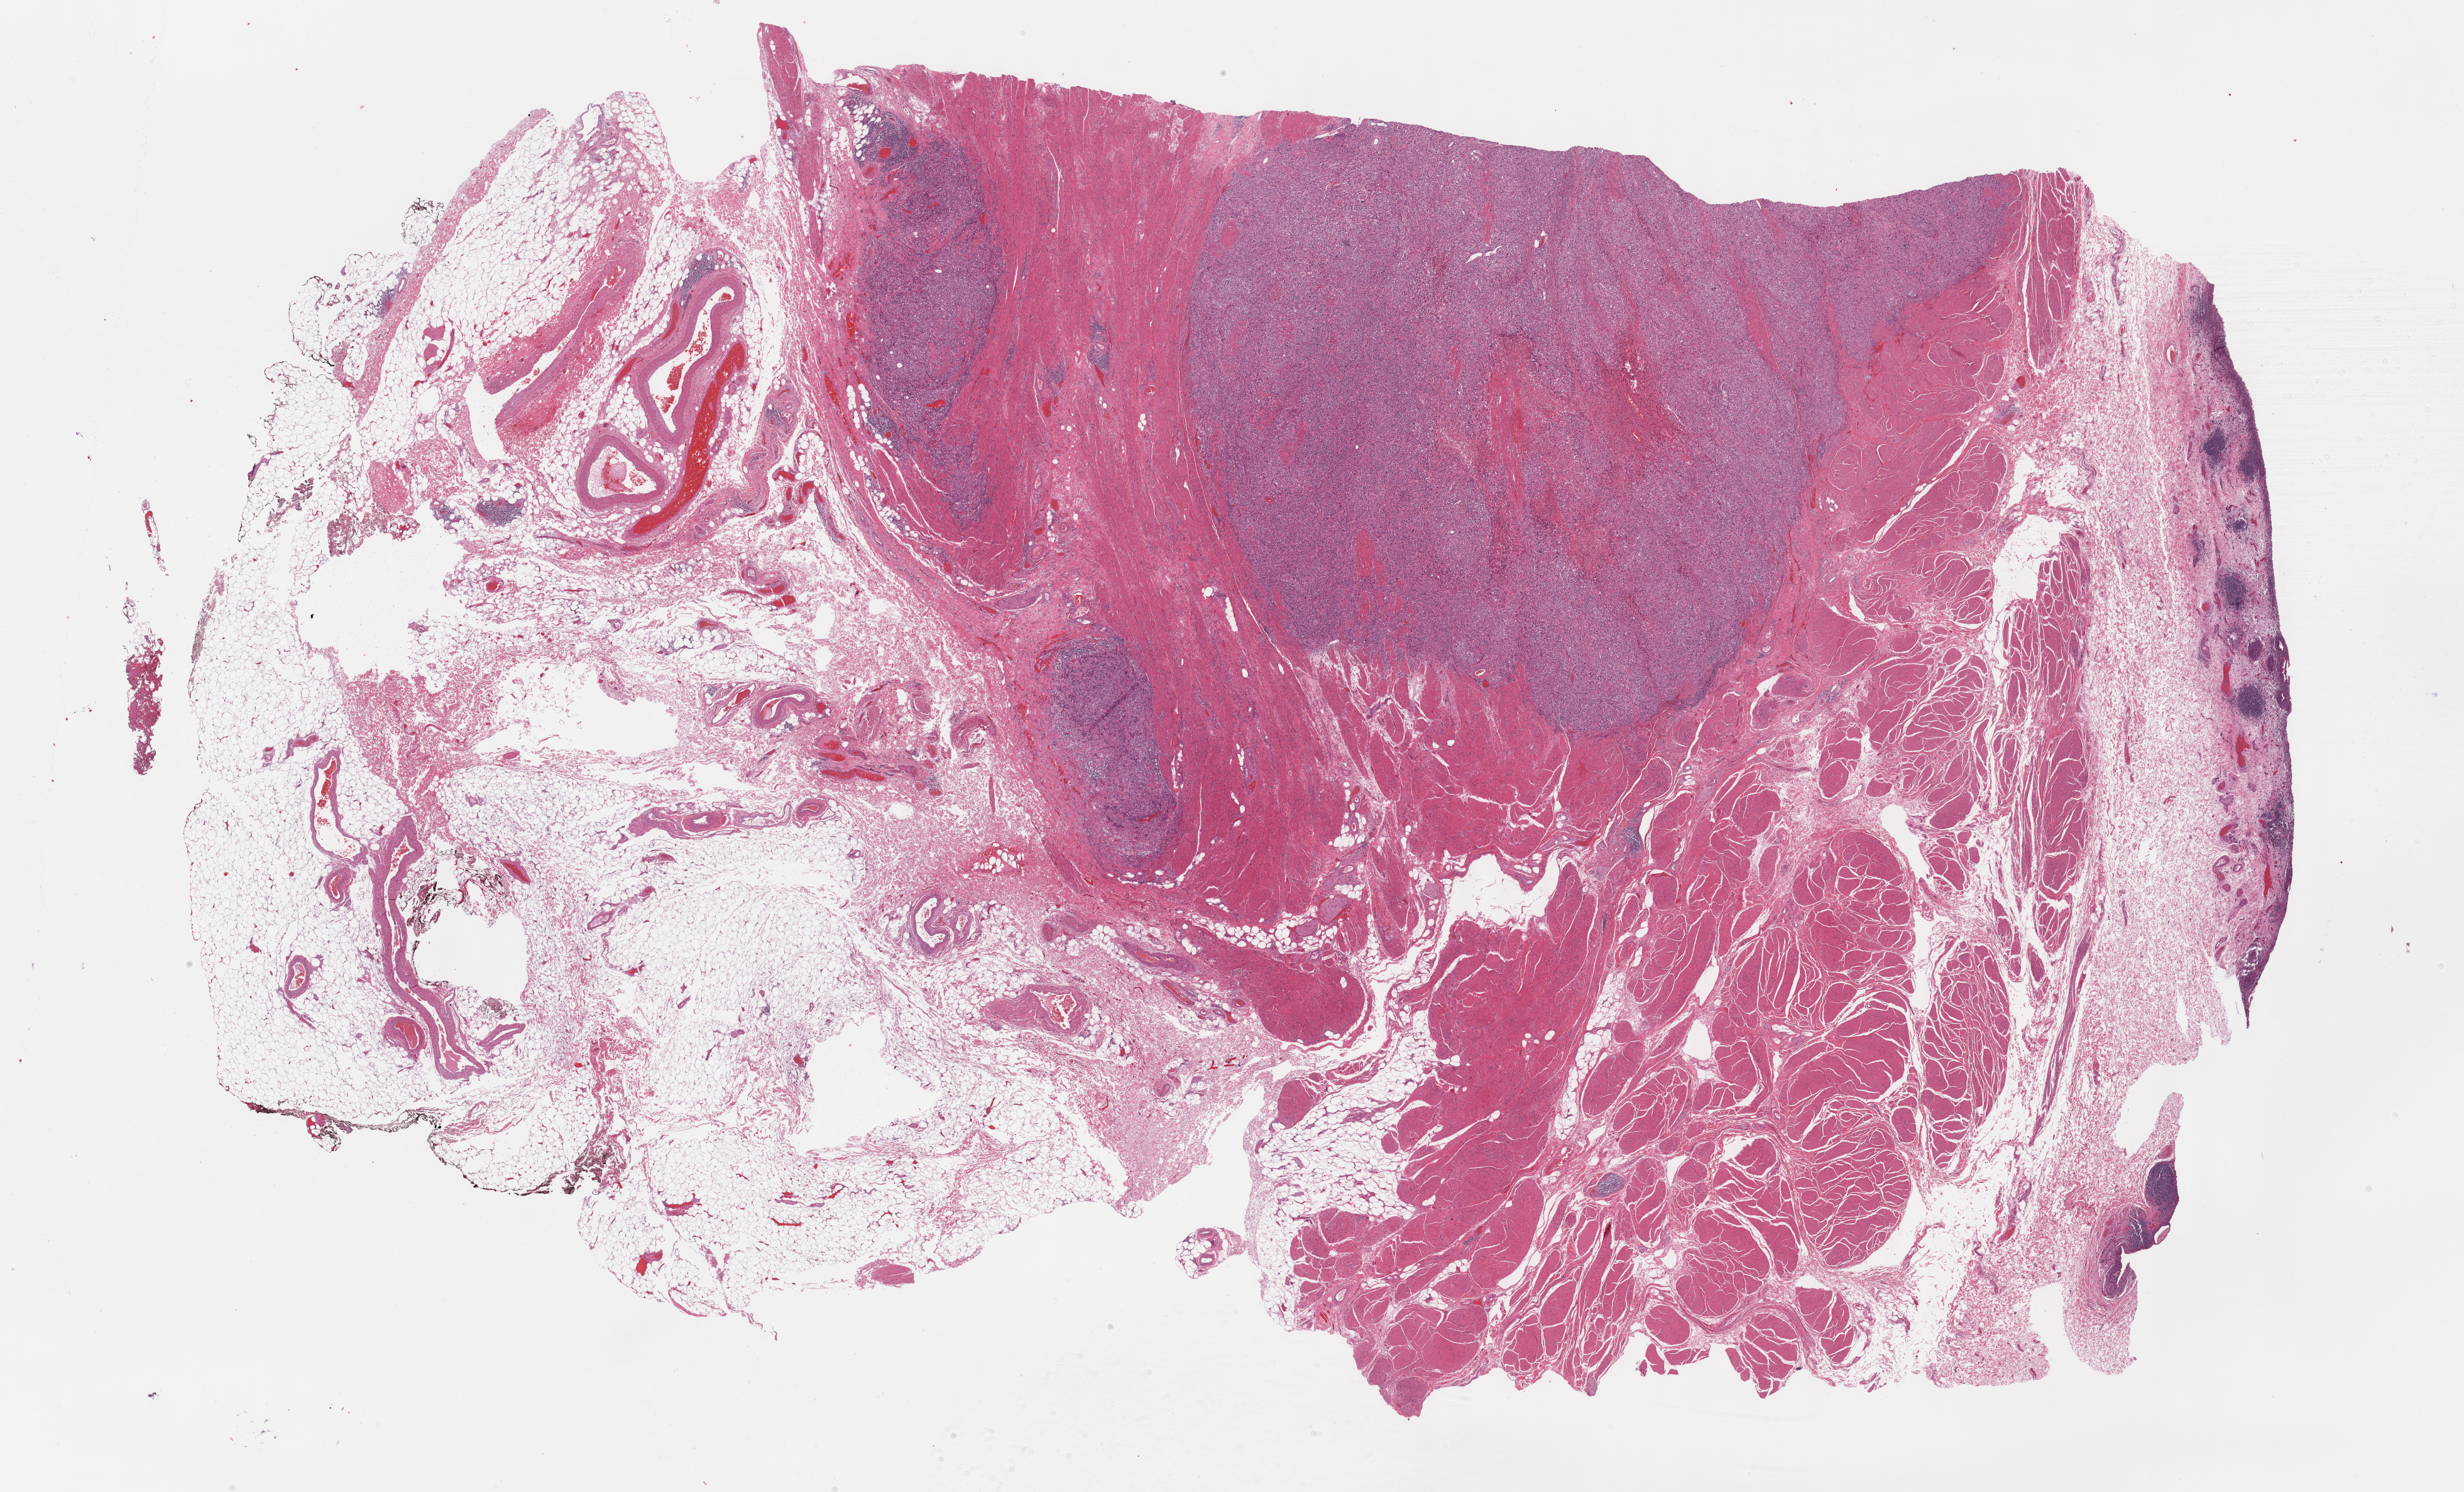
Whole-slide histology image, H&E, a low-resolution overview of the entire scanned area, about 31.7 x 19.2 mm, FFPE section, primary tumour sample from the bladder. Male patient; age at initial diagnosis 84 years. Histologic grade: high grade.
* AJCC pathologic stage: III (7th edition)
* diagnosis: Transitional cell carcinoma (lateral wall of bladder)
* lymph nodes positive (case pathology): 0 of 40 examined